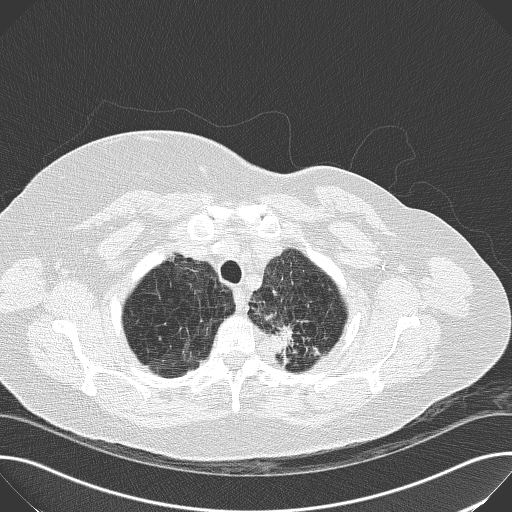
Chest CT (low-dose screening protocol), one axial image. First (baseline) screen. Lung window (W 1500 / L -600 HU). 2 mm slice thickness. 512 × 512 image matrix. Female participant, aged 56 years at enrolment.
• Expert reader's lesion annotation, bounding box (x1, y1, x2, y2) in pixels: (248, 304, 316, 372).
• Reader record for this screening exam (exam-level; its link to the box is not recorded): non-calcified nodule or mass ≥4 mm, left upper lobe, 19 × 17 mm, spiculated (stellate) margins, soft tissue attenuation.
• Participant outcome: lung cancer diagnosed 70 days after this screen — mucin-producing adenocarcinoma, left upper lobe, well differentiated (G1), stage IIB (AJCC 6th edition), 30 mm at pathology.